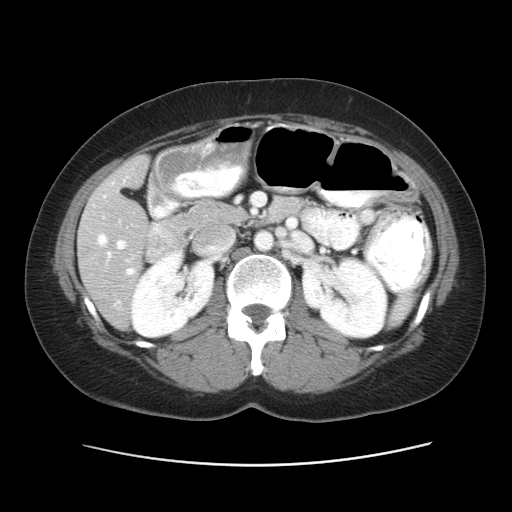
Contrast-enhanced abdominal CT, one axial slice. Slice 25 of 52 in the series (ordered by position). Reconstruction kernel STANDARD. 120 kVp. Intravenous contrast given. Soft-tissue window (W 400 / L 40 HU). 5 mm slice thickness. 512 × 512 image matrix, field of view 362 × 362 mm. Female patient, age 48 years. From the clinical record (not read from this slice): diagnosis: colorectal cancer liver metastases, imaged before liver resection; multiple liver metastases: yes.
Outlined on this slice (outlined manually by an expert reader):
- hepatic veins: box from (x=98, y=235) to (x=134, y=275) px
- liver: (x=79, y=157)–(x=149, y=328)
- portal vein (with intrahepatic branches): (x=117, y=240)–(x=126, y=249)
- liver metastasis: (x=79, y=246)–(x=93, y=259)